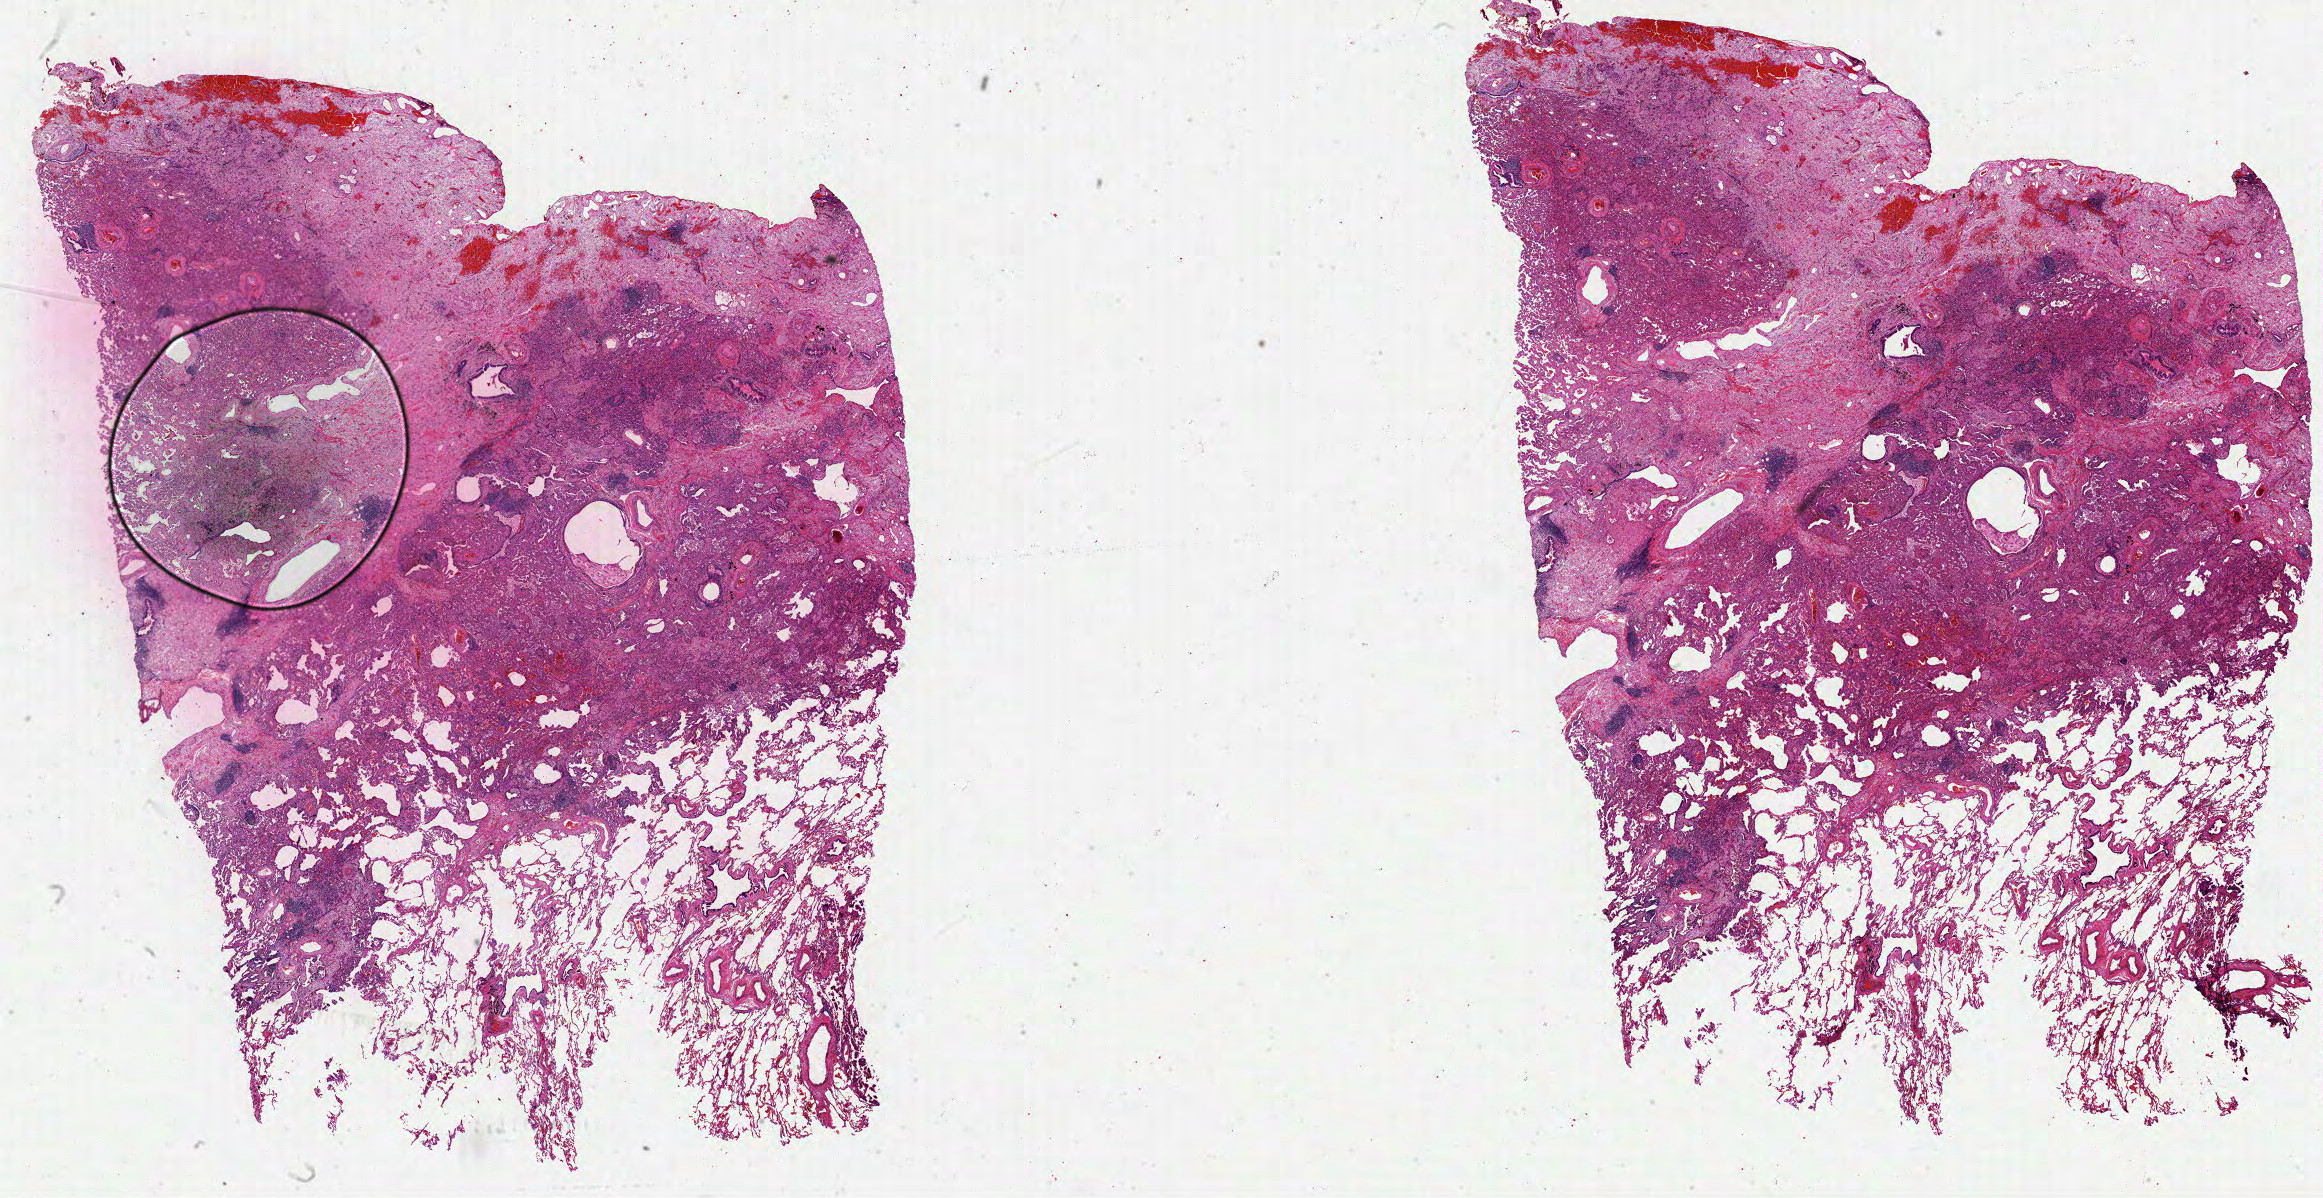
Whole-slide histology image, H&E-stained, a low-resolution overview of the entire scanned area, about 37.5 x 19.3 mm. Formalin-fixed paraffin-embedded (FFPE) diagnostic section. Primary tumour sample from the lung. Patient: male, age at initial diagnosis 82 years.
• AJCC pathologic stage: IIIA (7th edition)
• pathologic diagnosis: Papillary adenocarcinoma, NOS (upper lobe, lung)
• TNM: T2a N2 M0